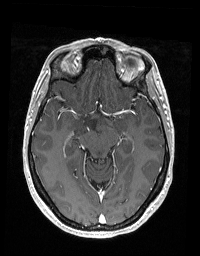
Brain MRI from a brain-tumour surgery series, one axial slice. Slice 112 of 192 in the series (ordered by position). T1-weighted post-contrast. 200 × 256 image matrix, field of view 195 × 250 mm. Case-level facts recorded for this patient, not image findings: histopathology: Glioblastoma; WHO grade: 2; IDH mutation: no; tumour location: Right Skull Base Temporal.
Outlined on this slice (outlined manually by an expert reader):
- tumour: bounding box [x1, y1, x2, y2] px = [75, 117, 96, 135]